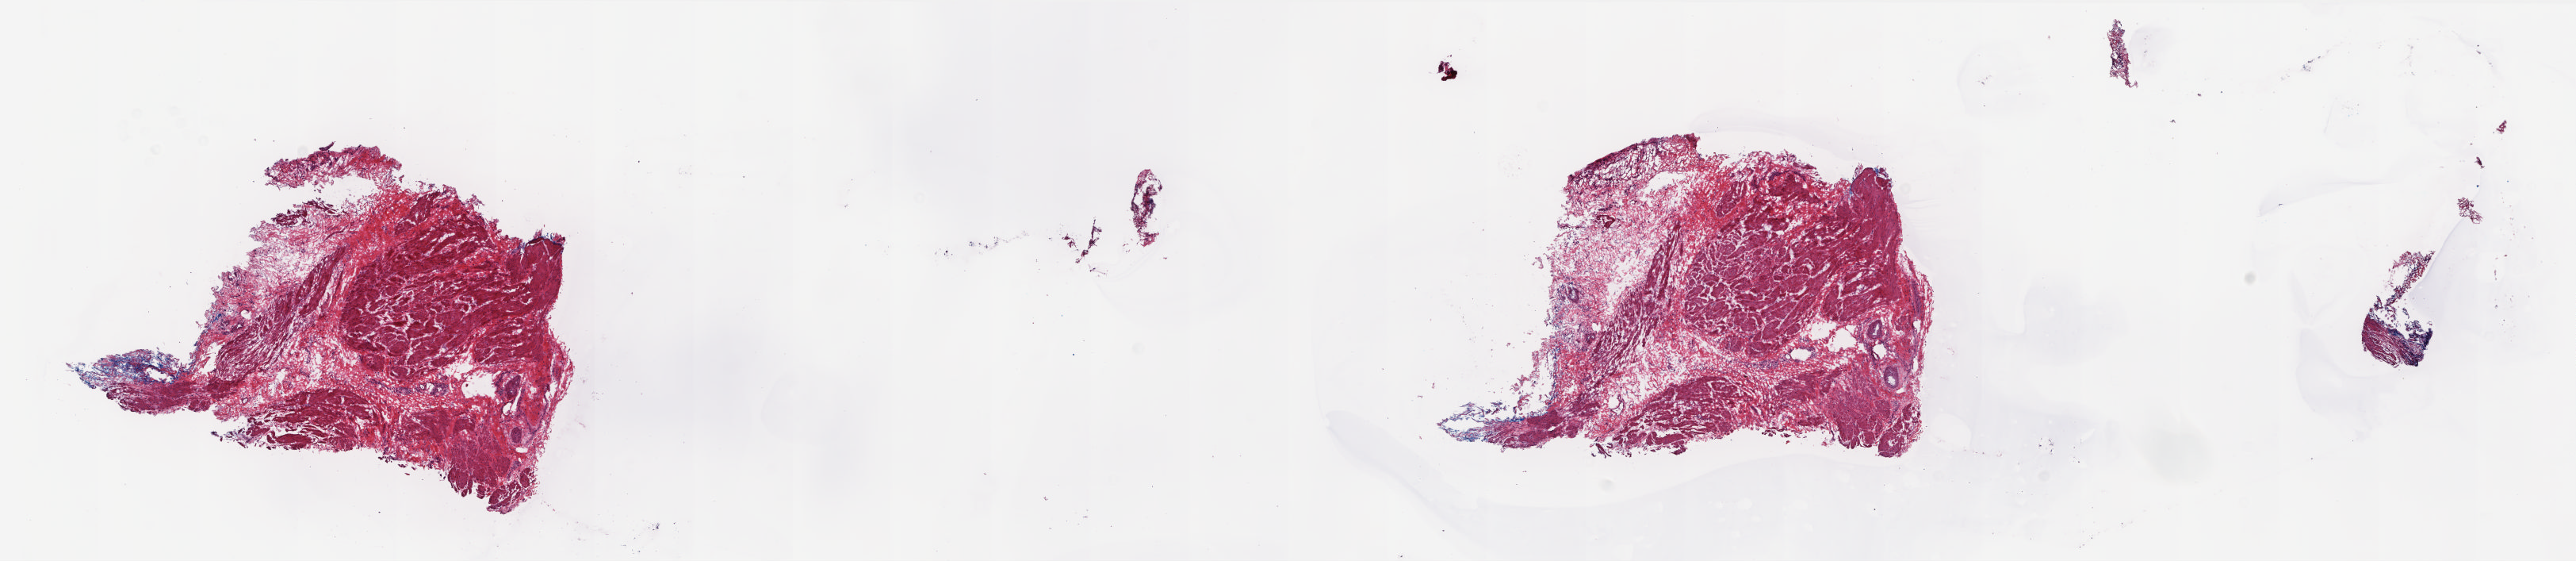
Digitized H&E tissue section (whole slide) — low-resolution overview of the scanned area, about 25.9 x 5.6 mm. Frozen section from the top of the tissue portion. Sample: solid tissue normal (non-tumour tissue), bladder. Female, age 80 years at initial diagnosis. Pathologist review of this section (percent, as recorded): tumour cells 0%, tumour nuclei 0%.
This section: solid tissue normal (non-tumour) sample from the same patient. Patient diagnosis: Transitional cell carcinoma.